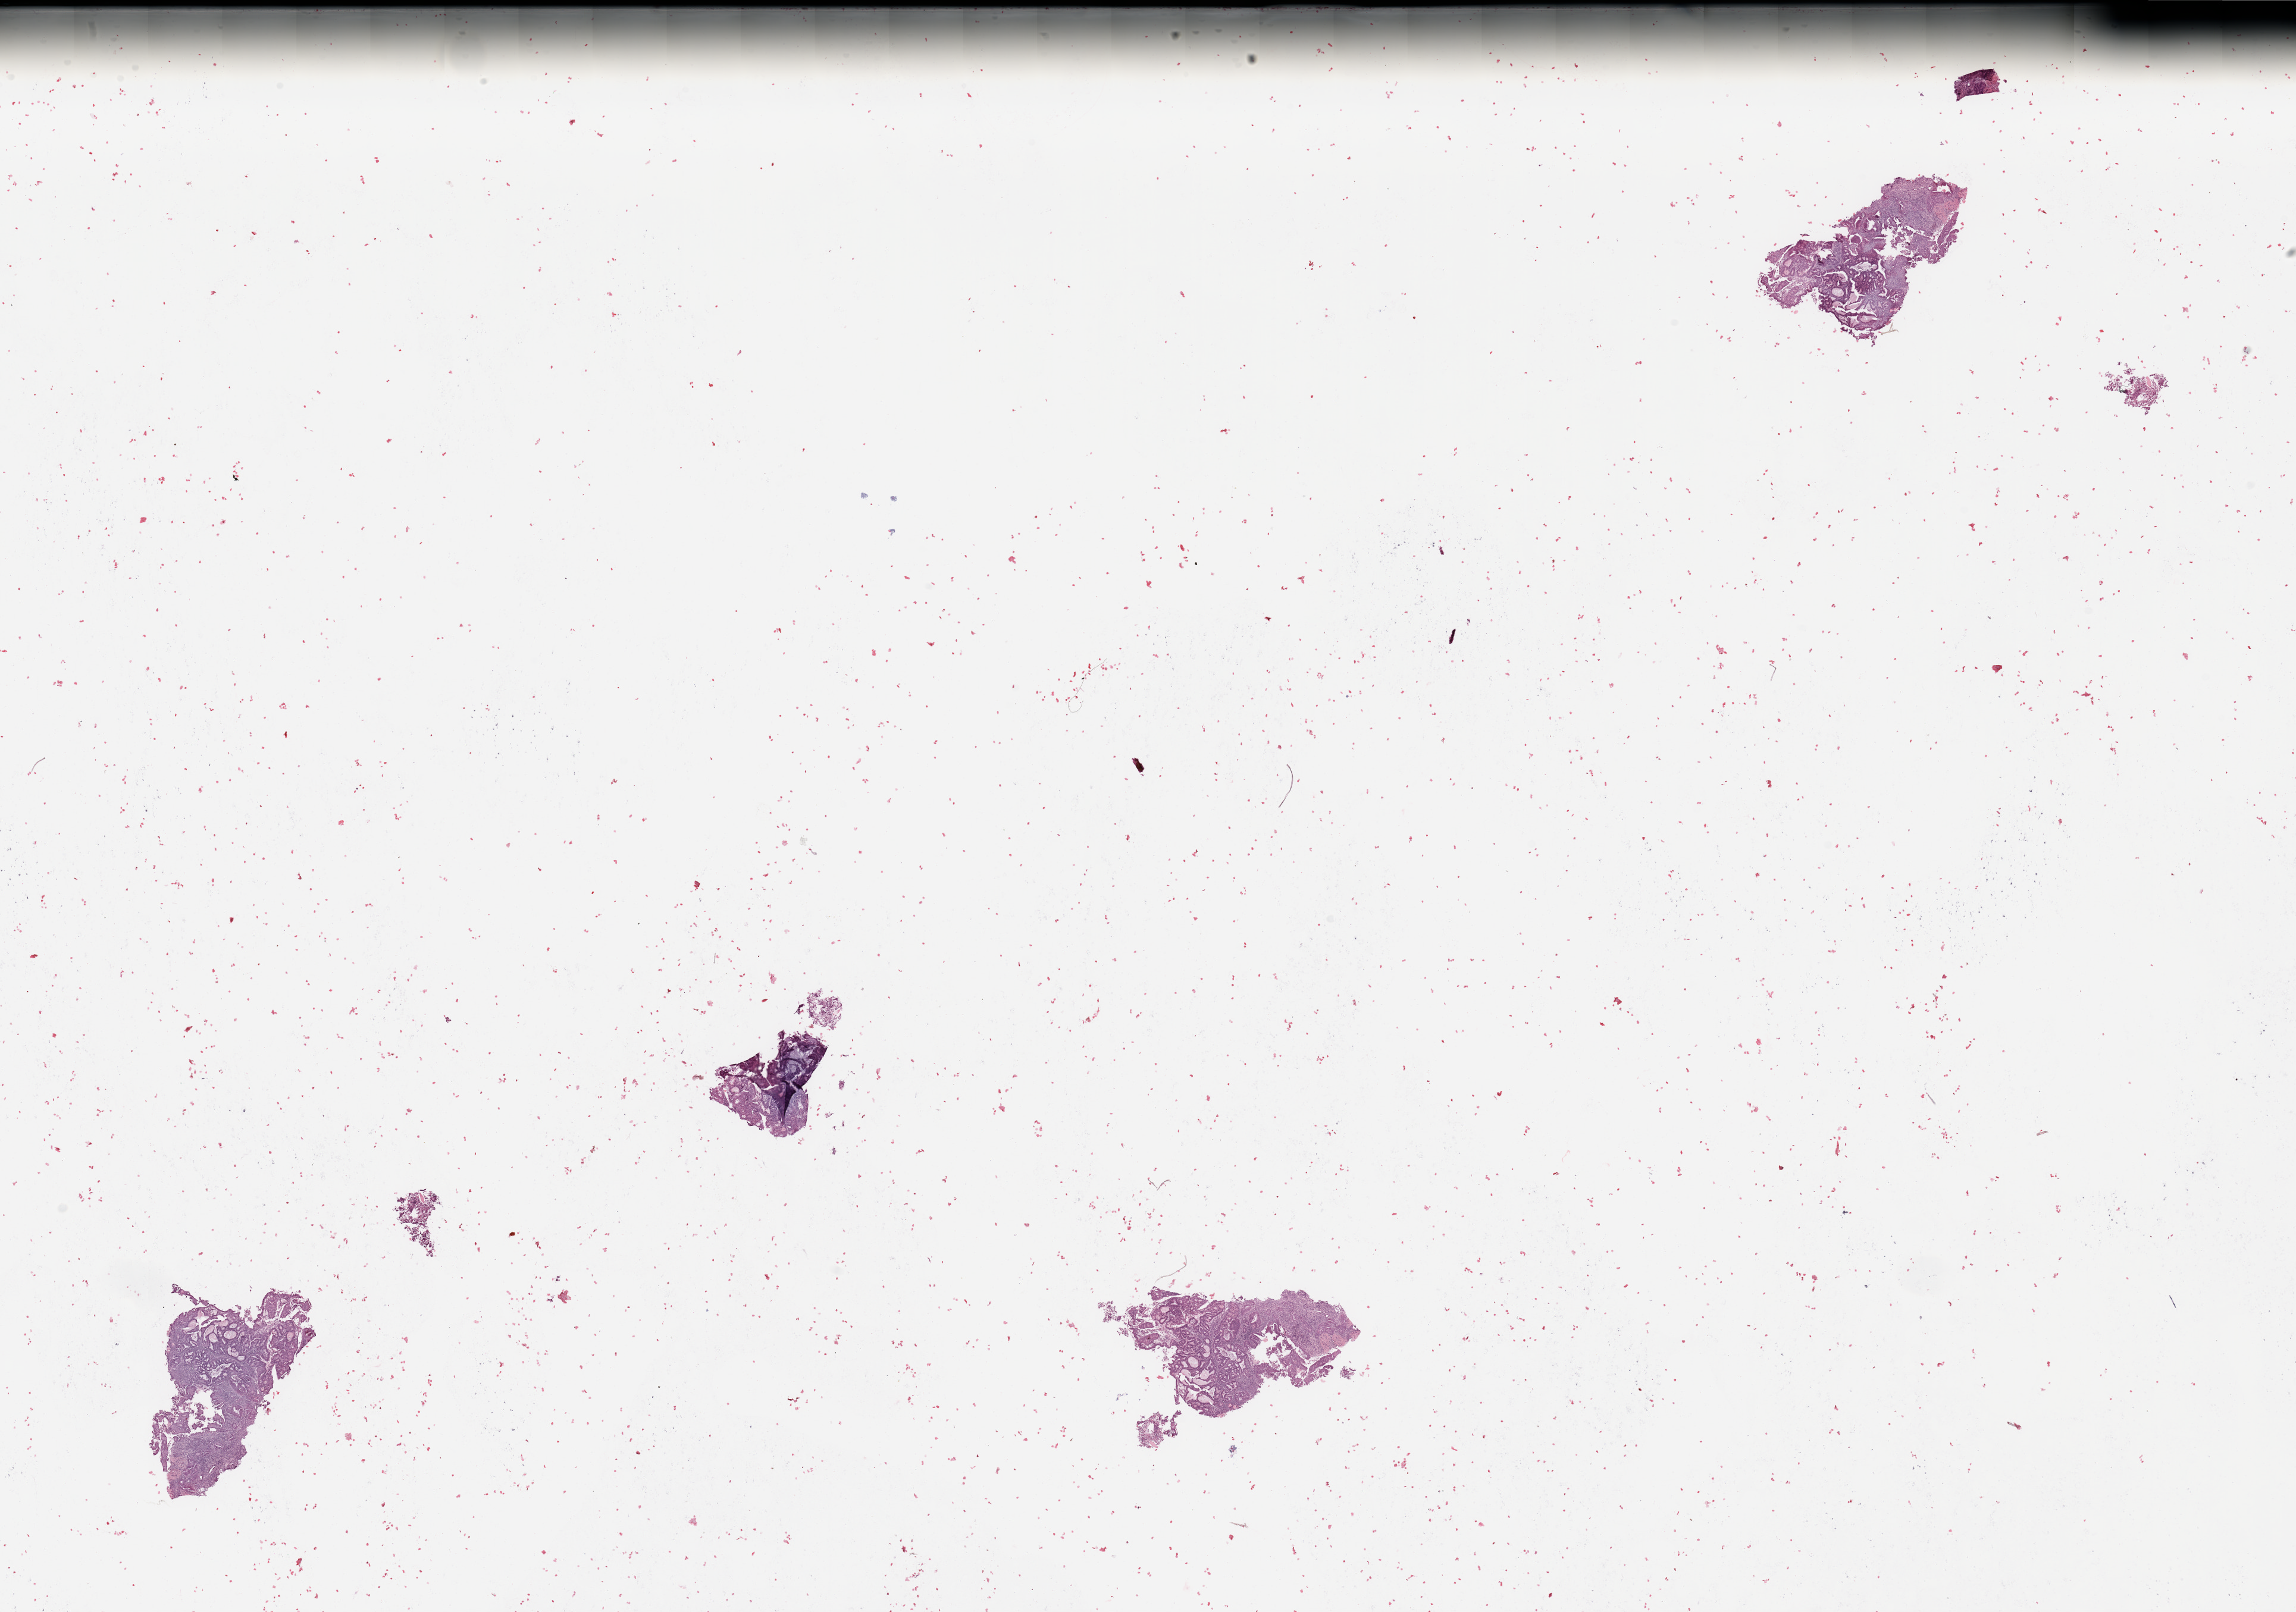
Hematoxylin and eosin (H&E) stained whole-slide image — shown as a low-resolution overview of the whole scanned area (about 30.5 x 21.4 mm, slide scanned at 20x). Tumour tissue sample, uterus. Patient: female, age 69 years. Histologic grade: G1 (well differentiated).
- histologic diagnosis: Endometrioid adenocarcinoma, NOS
- AJCC pathologic stage: II
- primary tumour site (as recorded): posterior endometrium